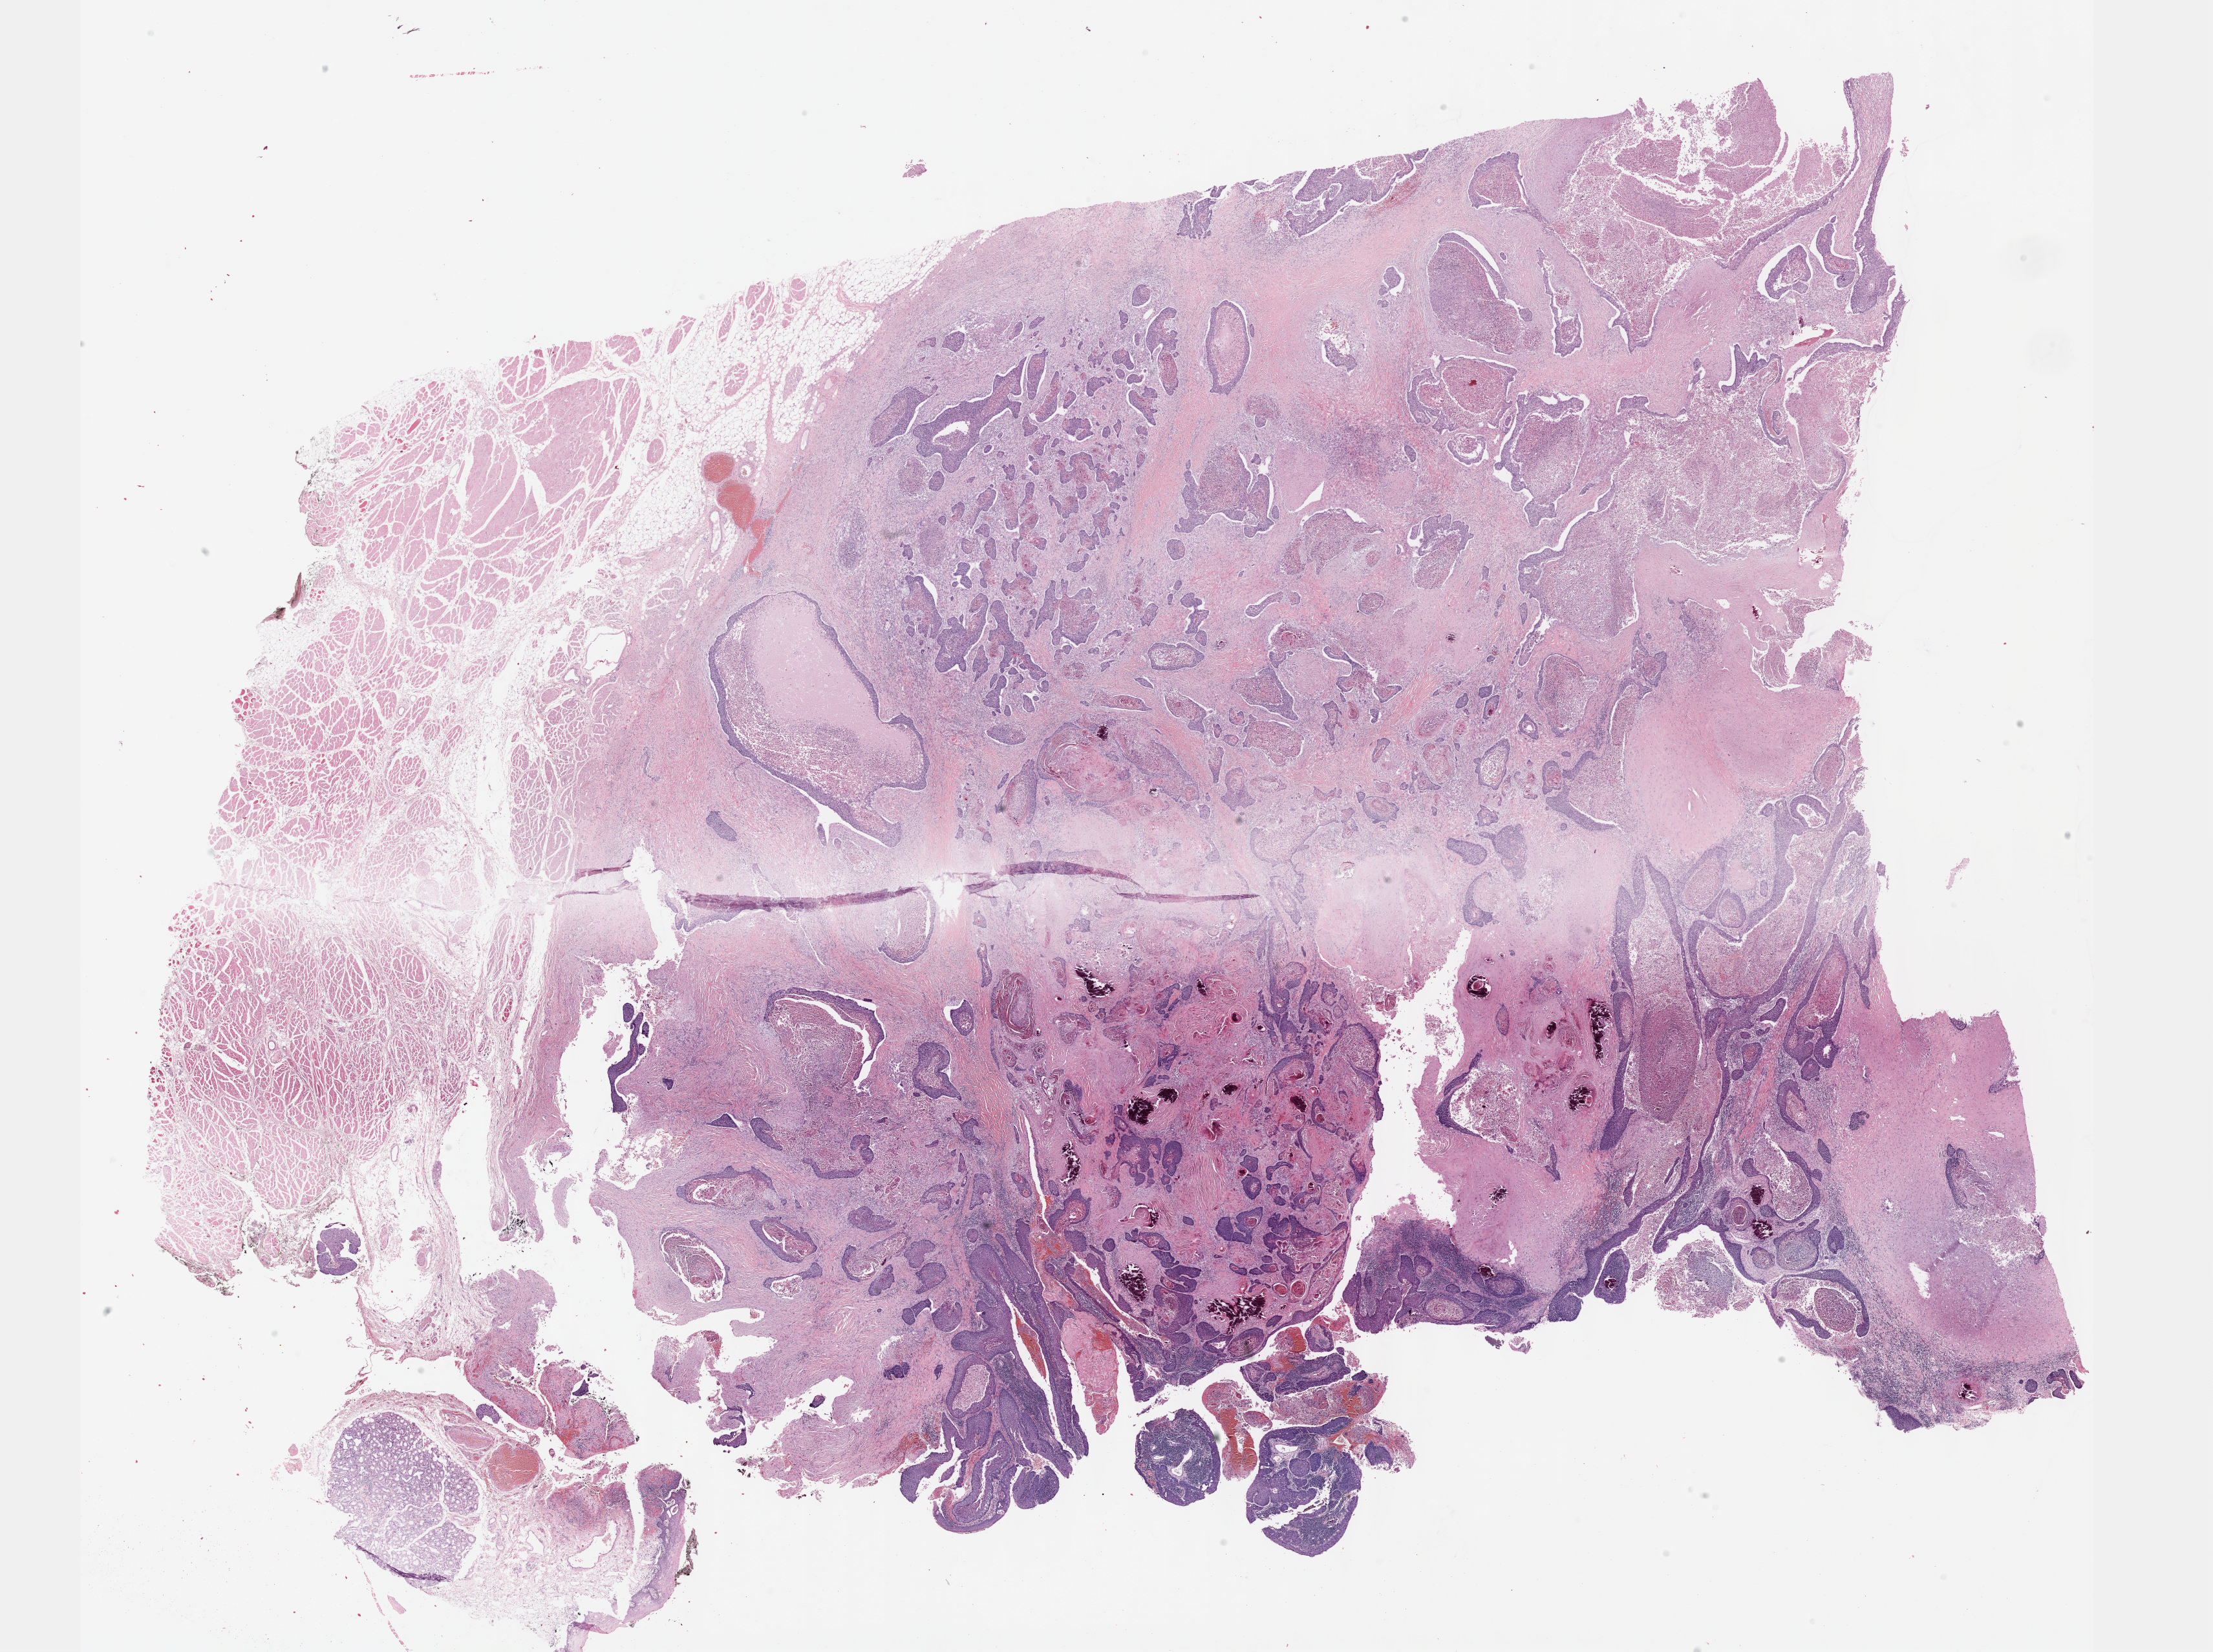
Whole-slide histology image, Hematoxylin and eosin (H&E) stained, a low-resolution overview of the entire scanned area, about 27.7 x 20.7 mm (acquisition: 40x scan); formalin-fixed paraffin-embedded (FFPE) diagnostic section; head and neck, primary tumour sample. Male patient; age at initial diagnosis 63 years. Histologic grade: G3 (poorly differentiated).
- AJCC pathologic stage: IVA (7th edition)
- pathologic diagnosis: Squamous cell carcinoma, NOS